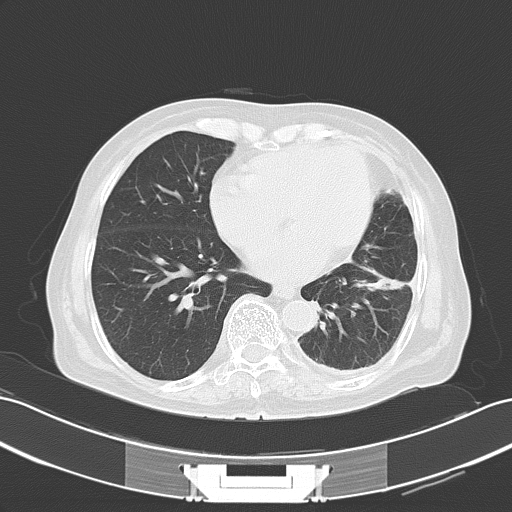
Chest CT, one axial slice. Slice 24 of 60 in the series (ordered by position). Lung window (W 1500 / L -600 HU). 512 × 512 image matrix, field of view 353 × 353 mm. Patient: female, 82 years. From the clinical record (not read from this slice): clinical TNM (as recorded): T1c N0 M1.
Annotated regions visible in this slice (rectangle marked by the reading radiologist):
- lung tumour (recorded histology: adenocarcinoma): bounding box <362,267,410,295> (left, top, right, bottom; pixels)